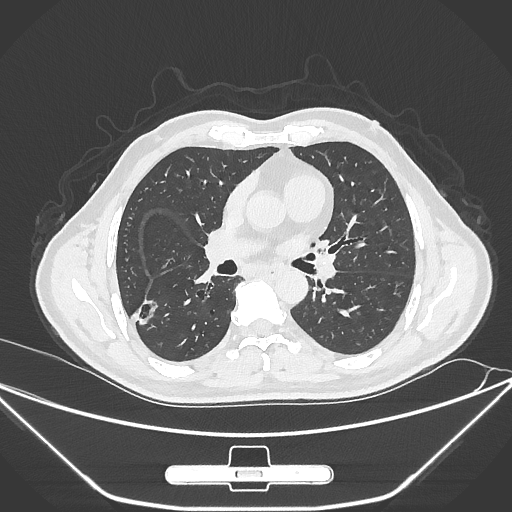
Chest CT, one axial slice. Slice 155 of 310 in the series (ordered by position). 120 kVp. Lung window (W 1500 / L -600 HU). 1 mm slice thickness. 512 × 512 image matrix, field of view 398 × 398 mm. Patient: male, 71 years. Case-level facts recorded for this patient, not image findings: clinical TNM (as recorded): T1c N0 M0.
Structures marked on this image (rectangle marked by the reading radiologist):
- lung tumour (recorded histology: adenocarcinoma): box from (x=129, y=286) to (x=157, y=333) px